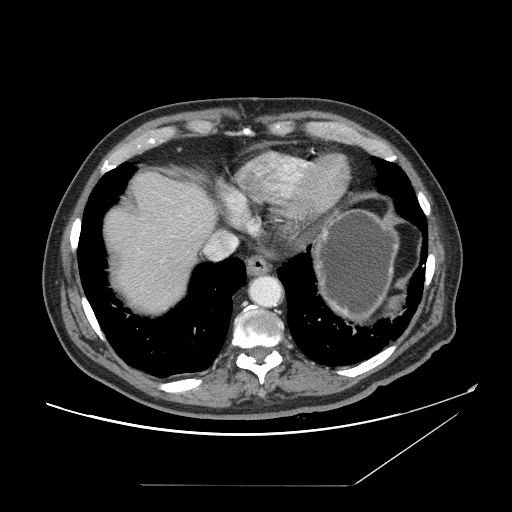
Contrast-enhanced abdominal CT, one axial slice; position 137 of 166 along the scan axis; intravenous contrast given; soft-tissue window (W 400 / L 40 HU); 512 × 512 image matrix, field of view 416 × 416 mm. Male patient, age 80 years. From the clinical record (not read from this slice): diagnosis: colorectal cancer liver metastases, imaged before liver resection; multiple liver metastases: no; largest metastasis: 2.2 cm; chemotherapy before resection: no.
Annotated regions visible in this slice (outlined manually by an expert reader):
- hepatic veins: bounding box [x1, y1, x2, y2] px = [206, 236, 237, 259]
- liver: [103, 173, 218, 316]
- planned liver remnant (the part of the liver to remain after resection): [102, 172, 218, 258]